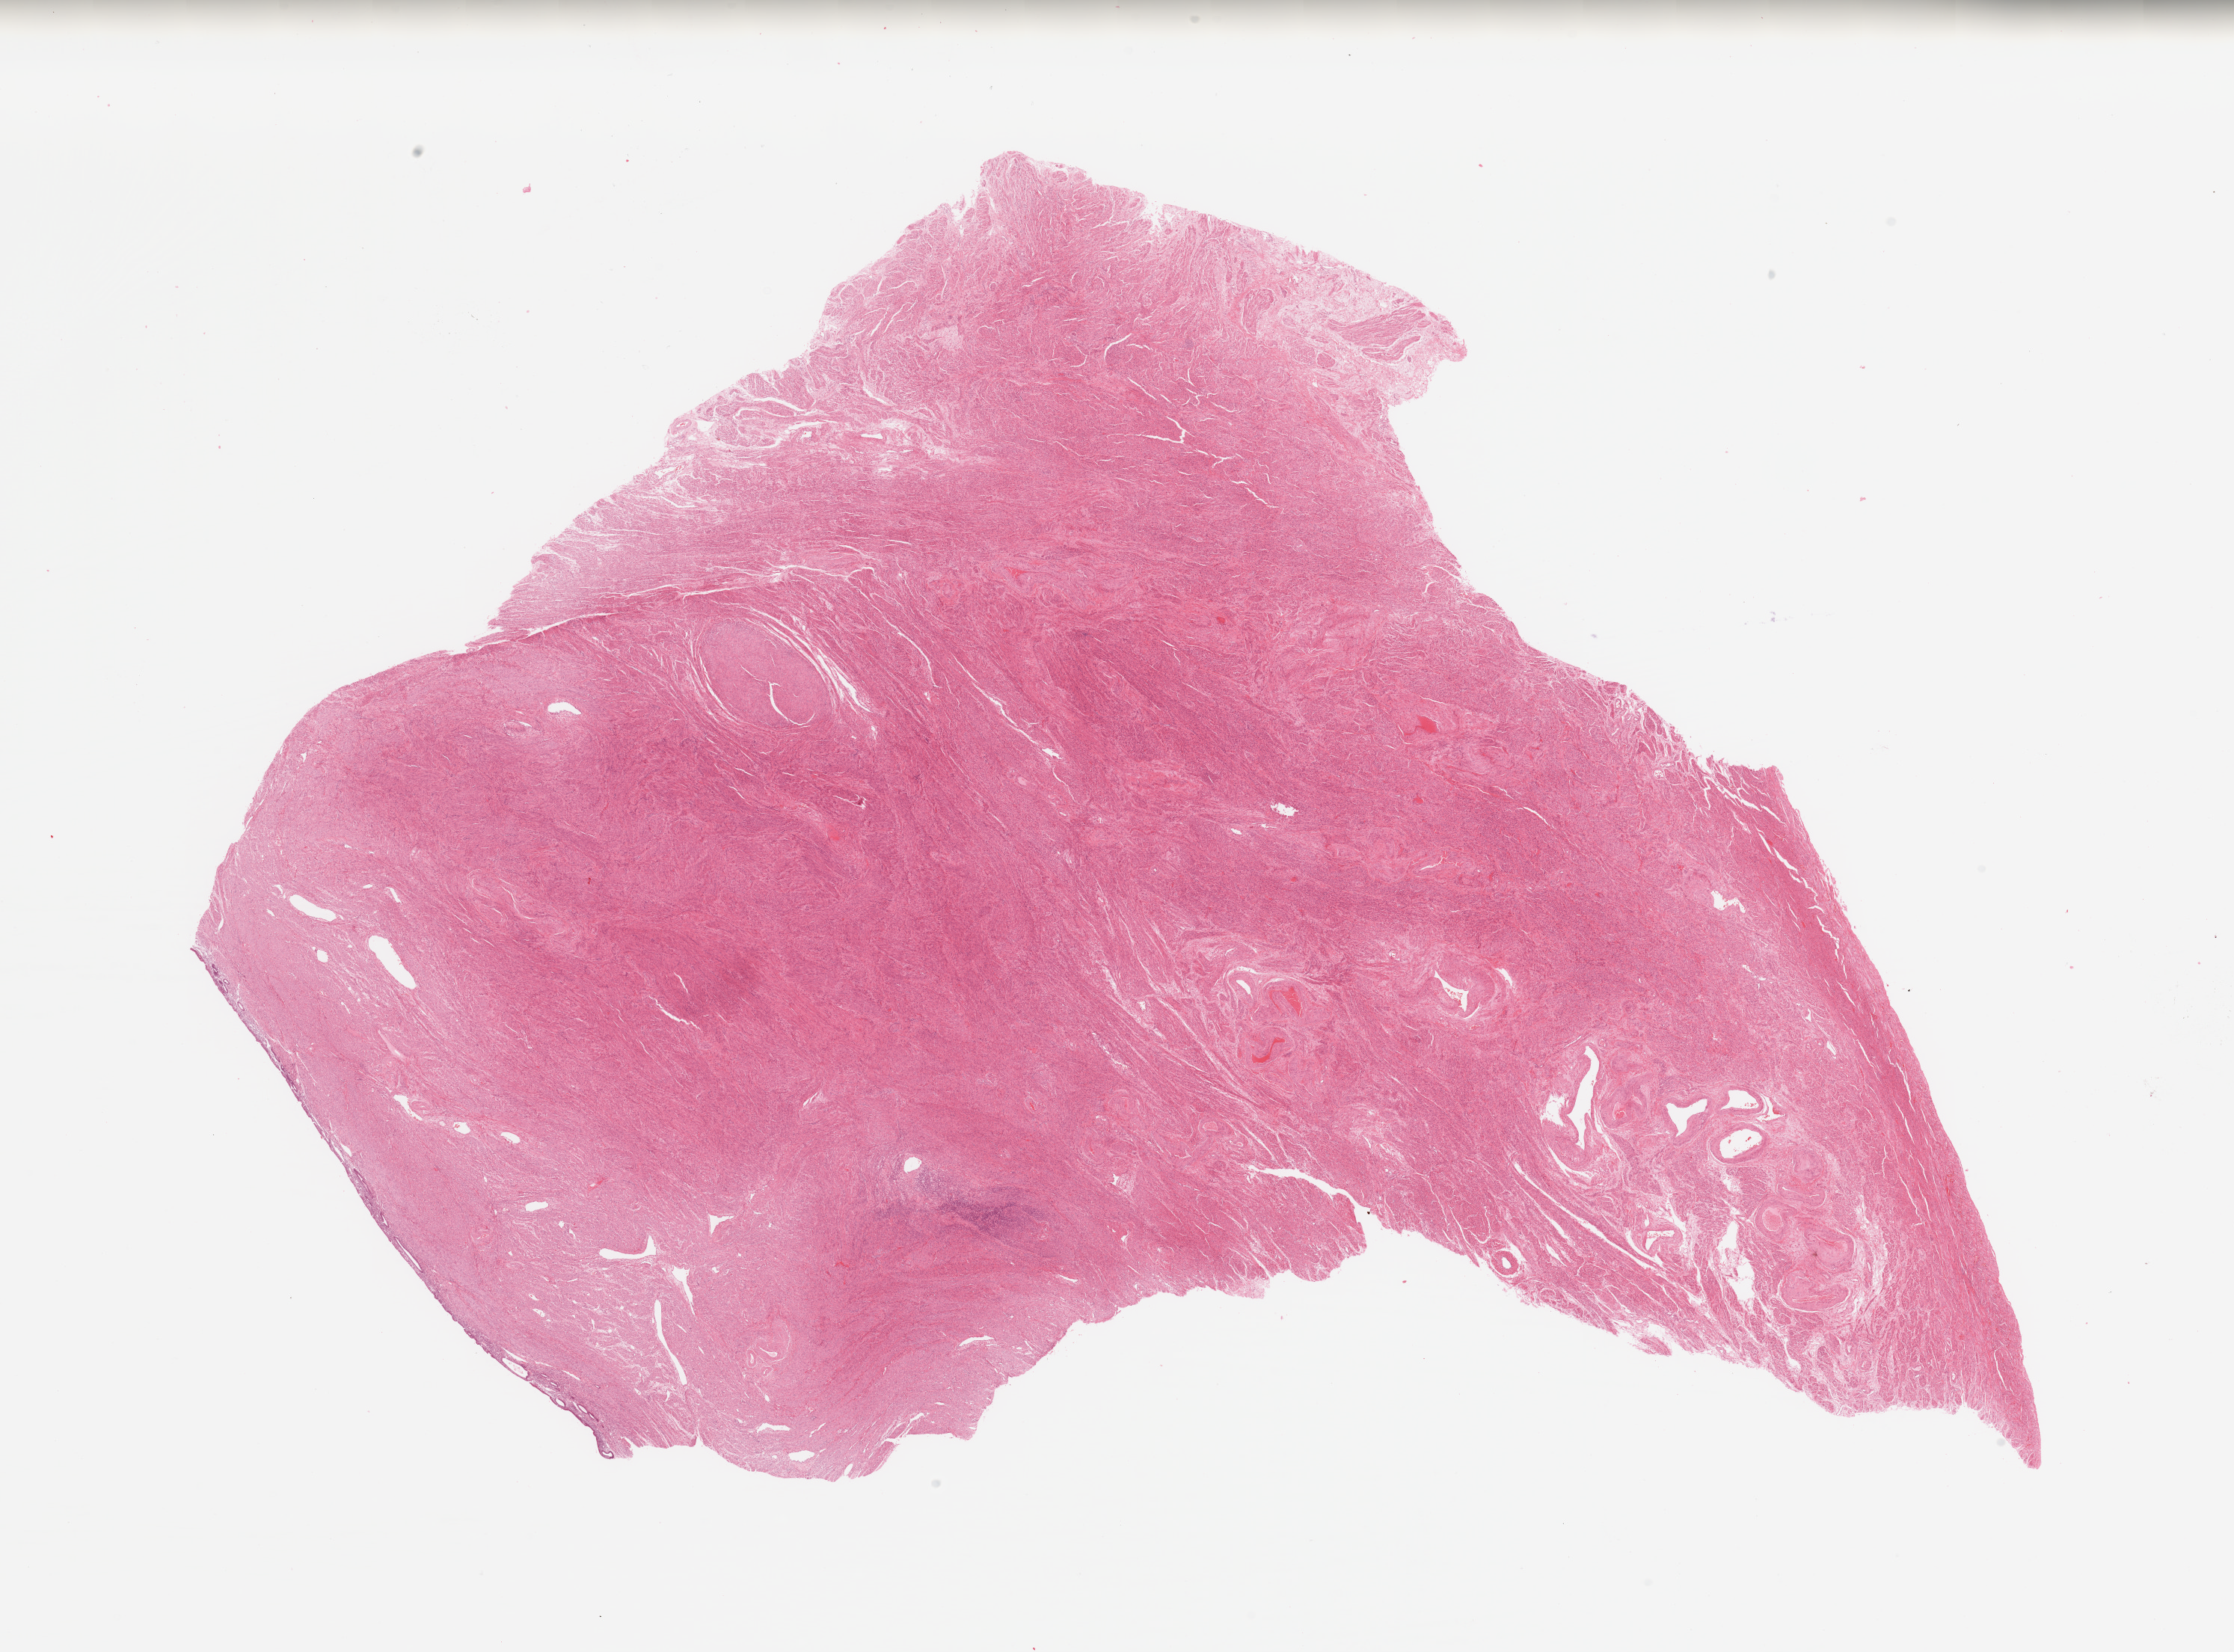
Digitized H&E-stained tissue section (whole slide) — shown as a low-resolution overview of the whole scanned area (about 23.6 x 17.5 mm, slide scanned at 20x); normal (non-tumour) tissue sample, sampled site: uterus. 77-year-old female patient.
* this section: normal (non-tumour) tissue from the same patient
* patient diagnosis: Endometrioid adenocarcinoma, NOS